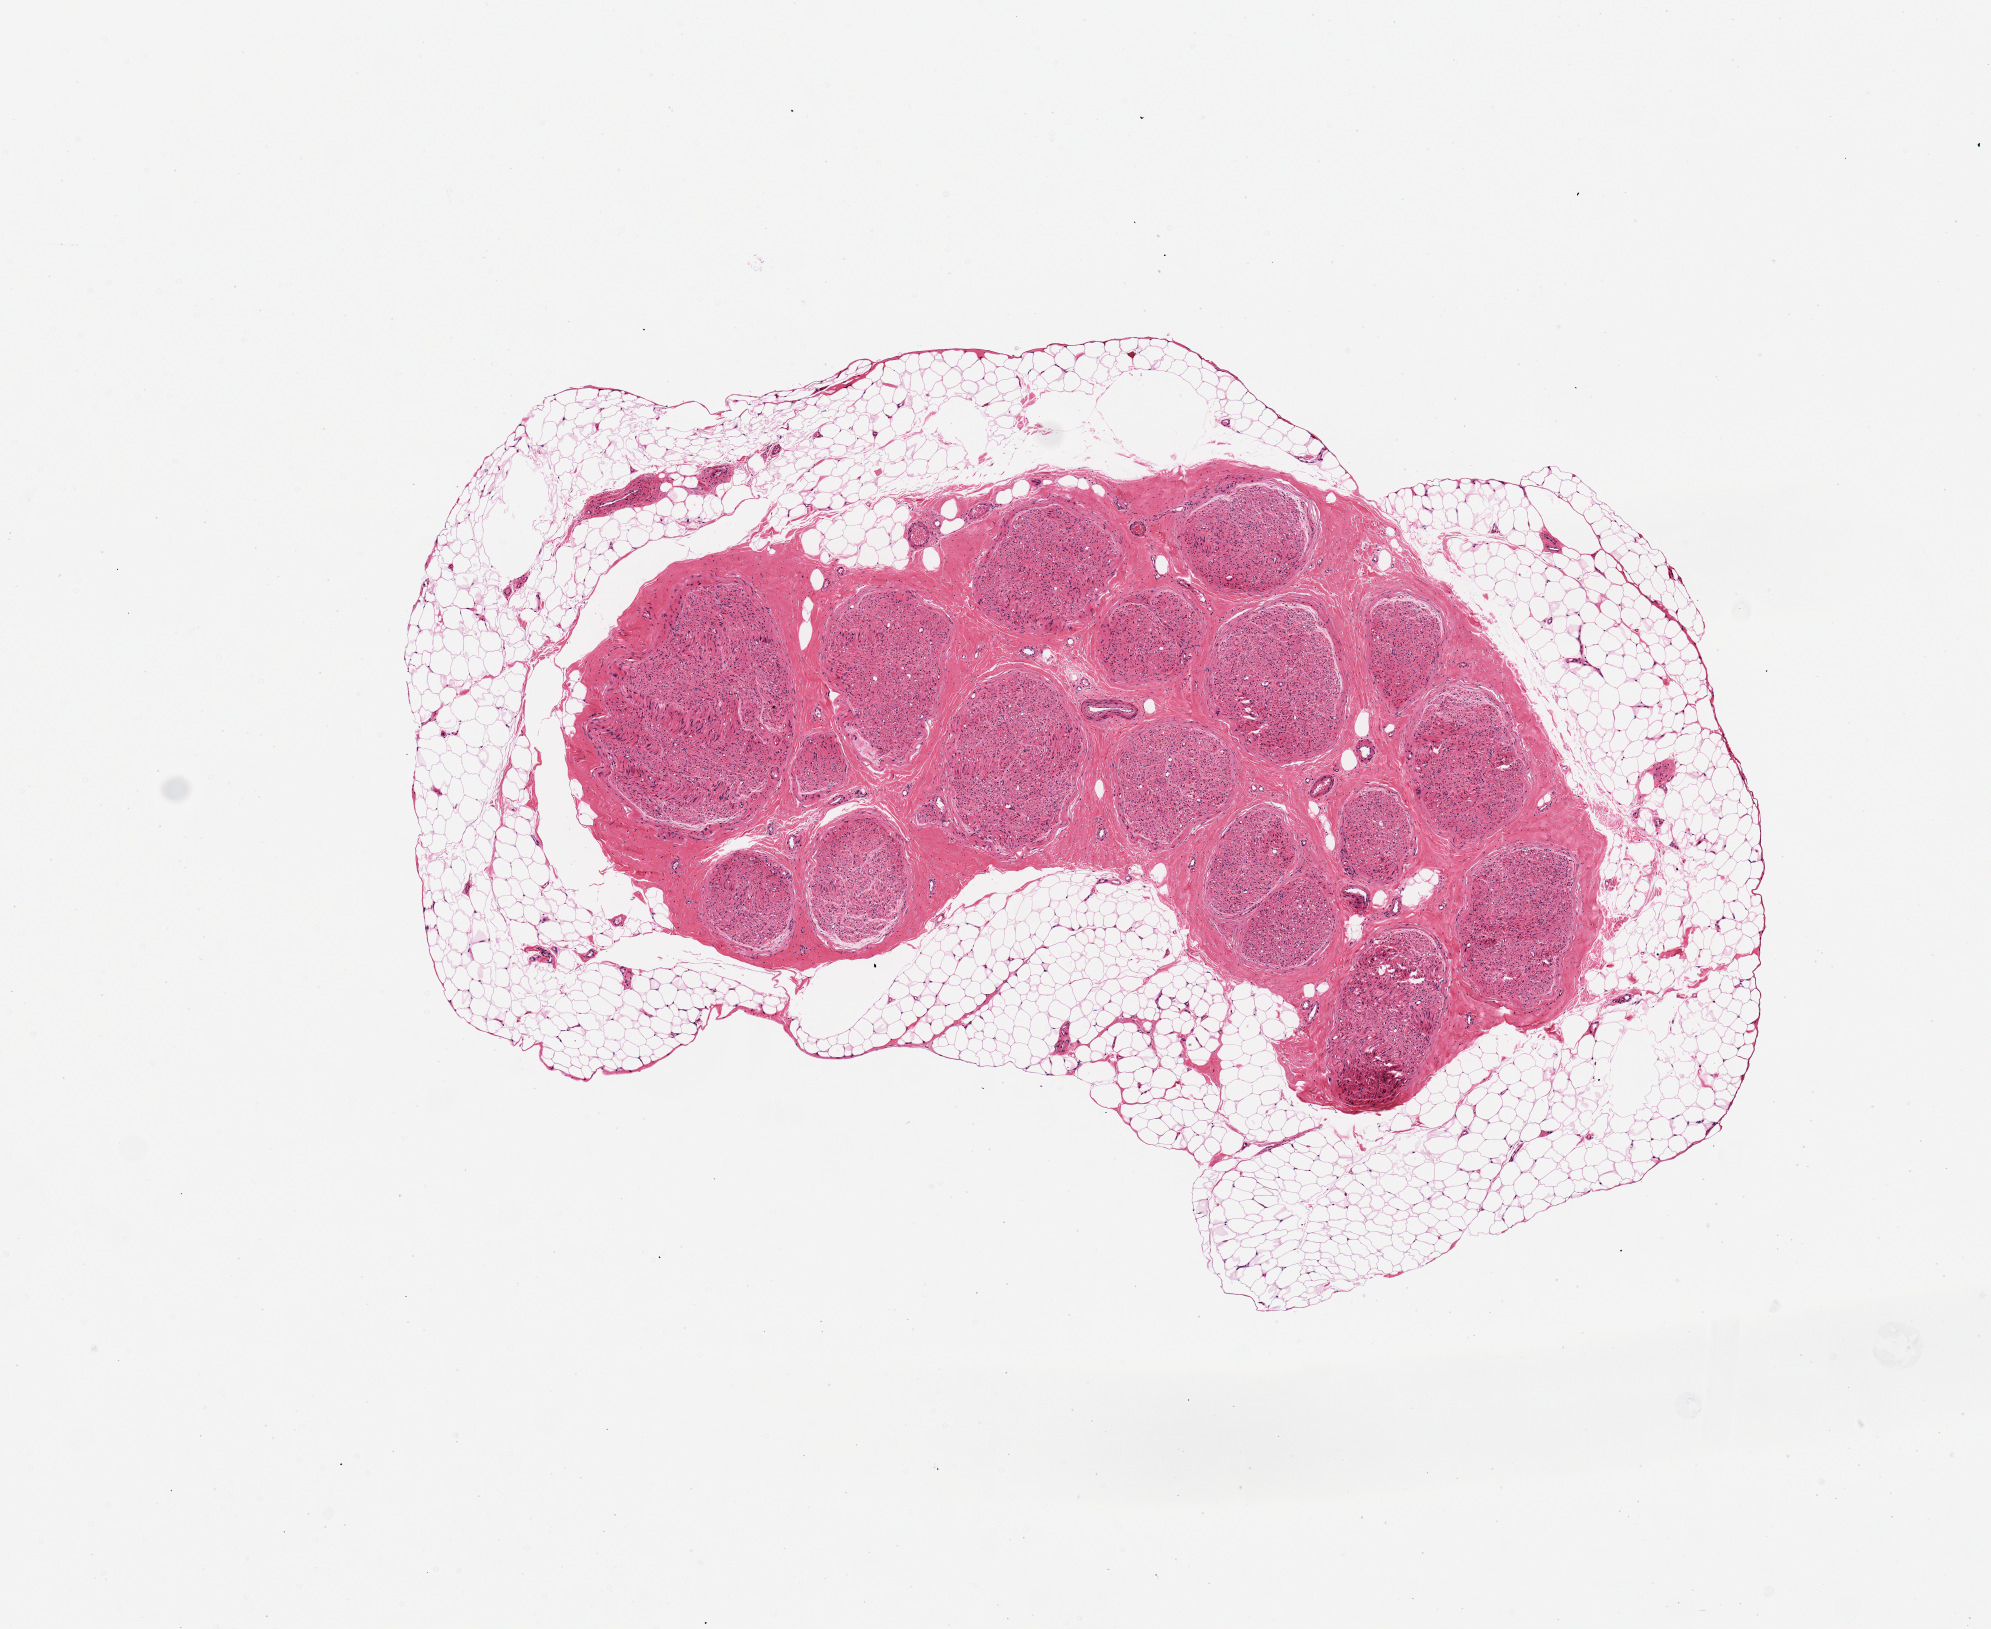
Whole-slide image, hematoxylin and eosin (H&E) stain — whole scanned area (about 7.9 x 6.4 mm) shown as a low-resolution overview; PAXgene-fixed, paraffin-embedded tissue; sampled site (target tissue): tibial nerve; donor tissue sample. Female donor.
Pathologist's review note for this sample: adequate for analysis.